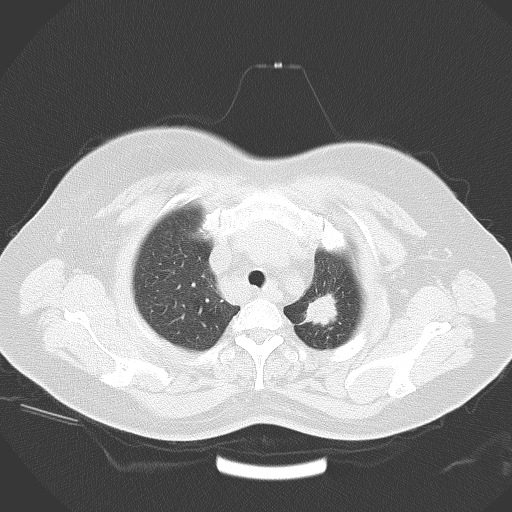
Chest CT, one axial slice. Slice 50 of 58 in the series (ordered by position). 120 kVp. Lung window (W 1500 / L -600 HU). 5 mm slice thickness. 512 × 512 image matrix, field of view 390 × 390 mm. Patient: female, 53 years. Case-level facts recorded for this patient, not image findings: clinical TNM (as recorded): T1c N3 M0.
Structures marked on this image (bounding box drawn by a radiologist):
- lung tumour (recorded histology: adenocarcinoma): bounding box [x1, y1, x2, y2] px = [295, 286, 344, 336]